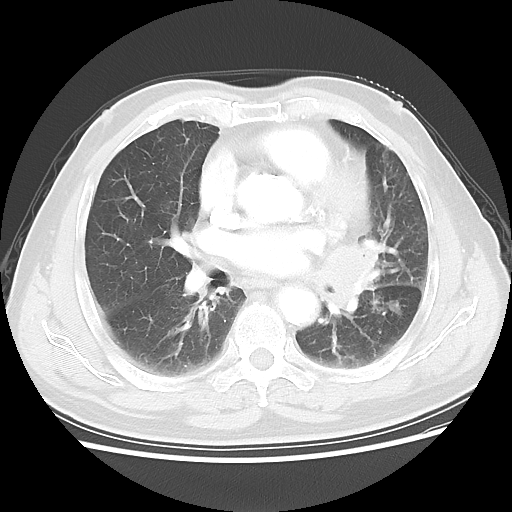
Chest CT, one axial slice; position 30 of 56 along the scan axis; reconstruction kernel LUNG; 120 kVp; lung window (W 1500 / L -600 HU); 512 × 512 image matrix, field of view 360 × 360 mm. Patient: male, 75 years. From the clinical record (not read from this slice): clinical TNM (as recorded): T3 N0 M0.
Annotated regions visible in this slice (rectangle marked by the reading radiologist):
- lung tumour (recorded histology: squamous cell carcinoma): box from (x=313, y=237) to (x=381, y=326) px